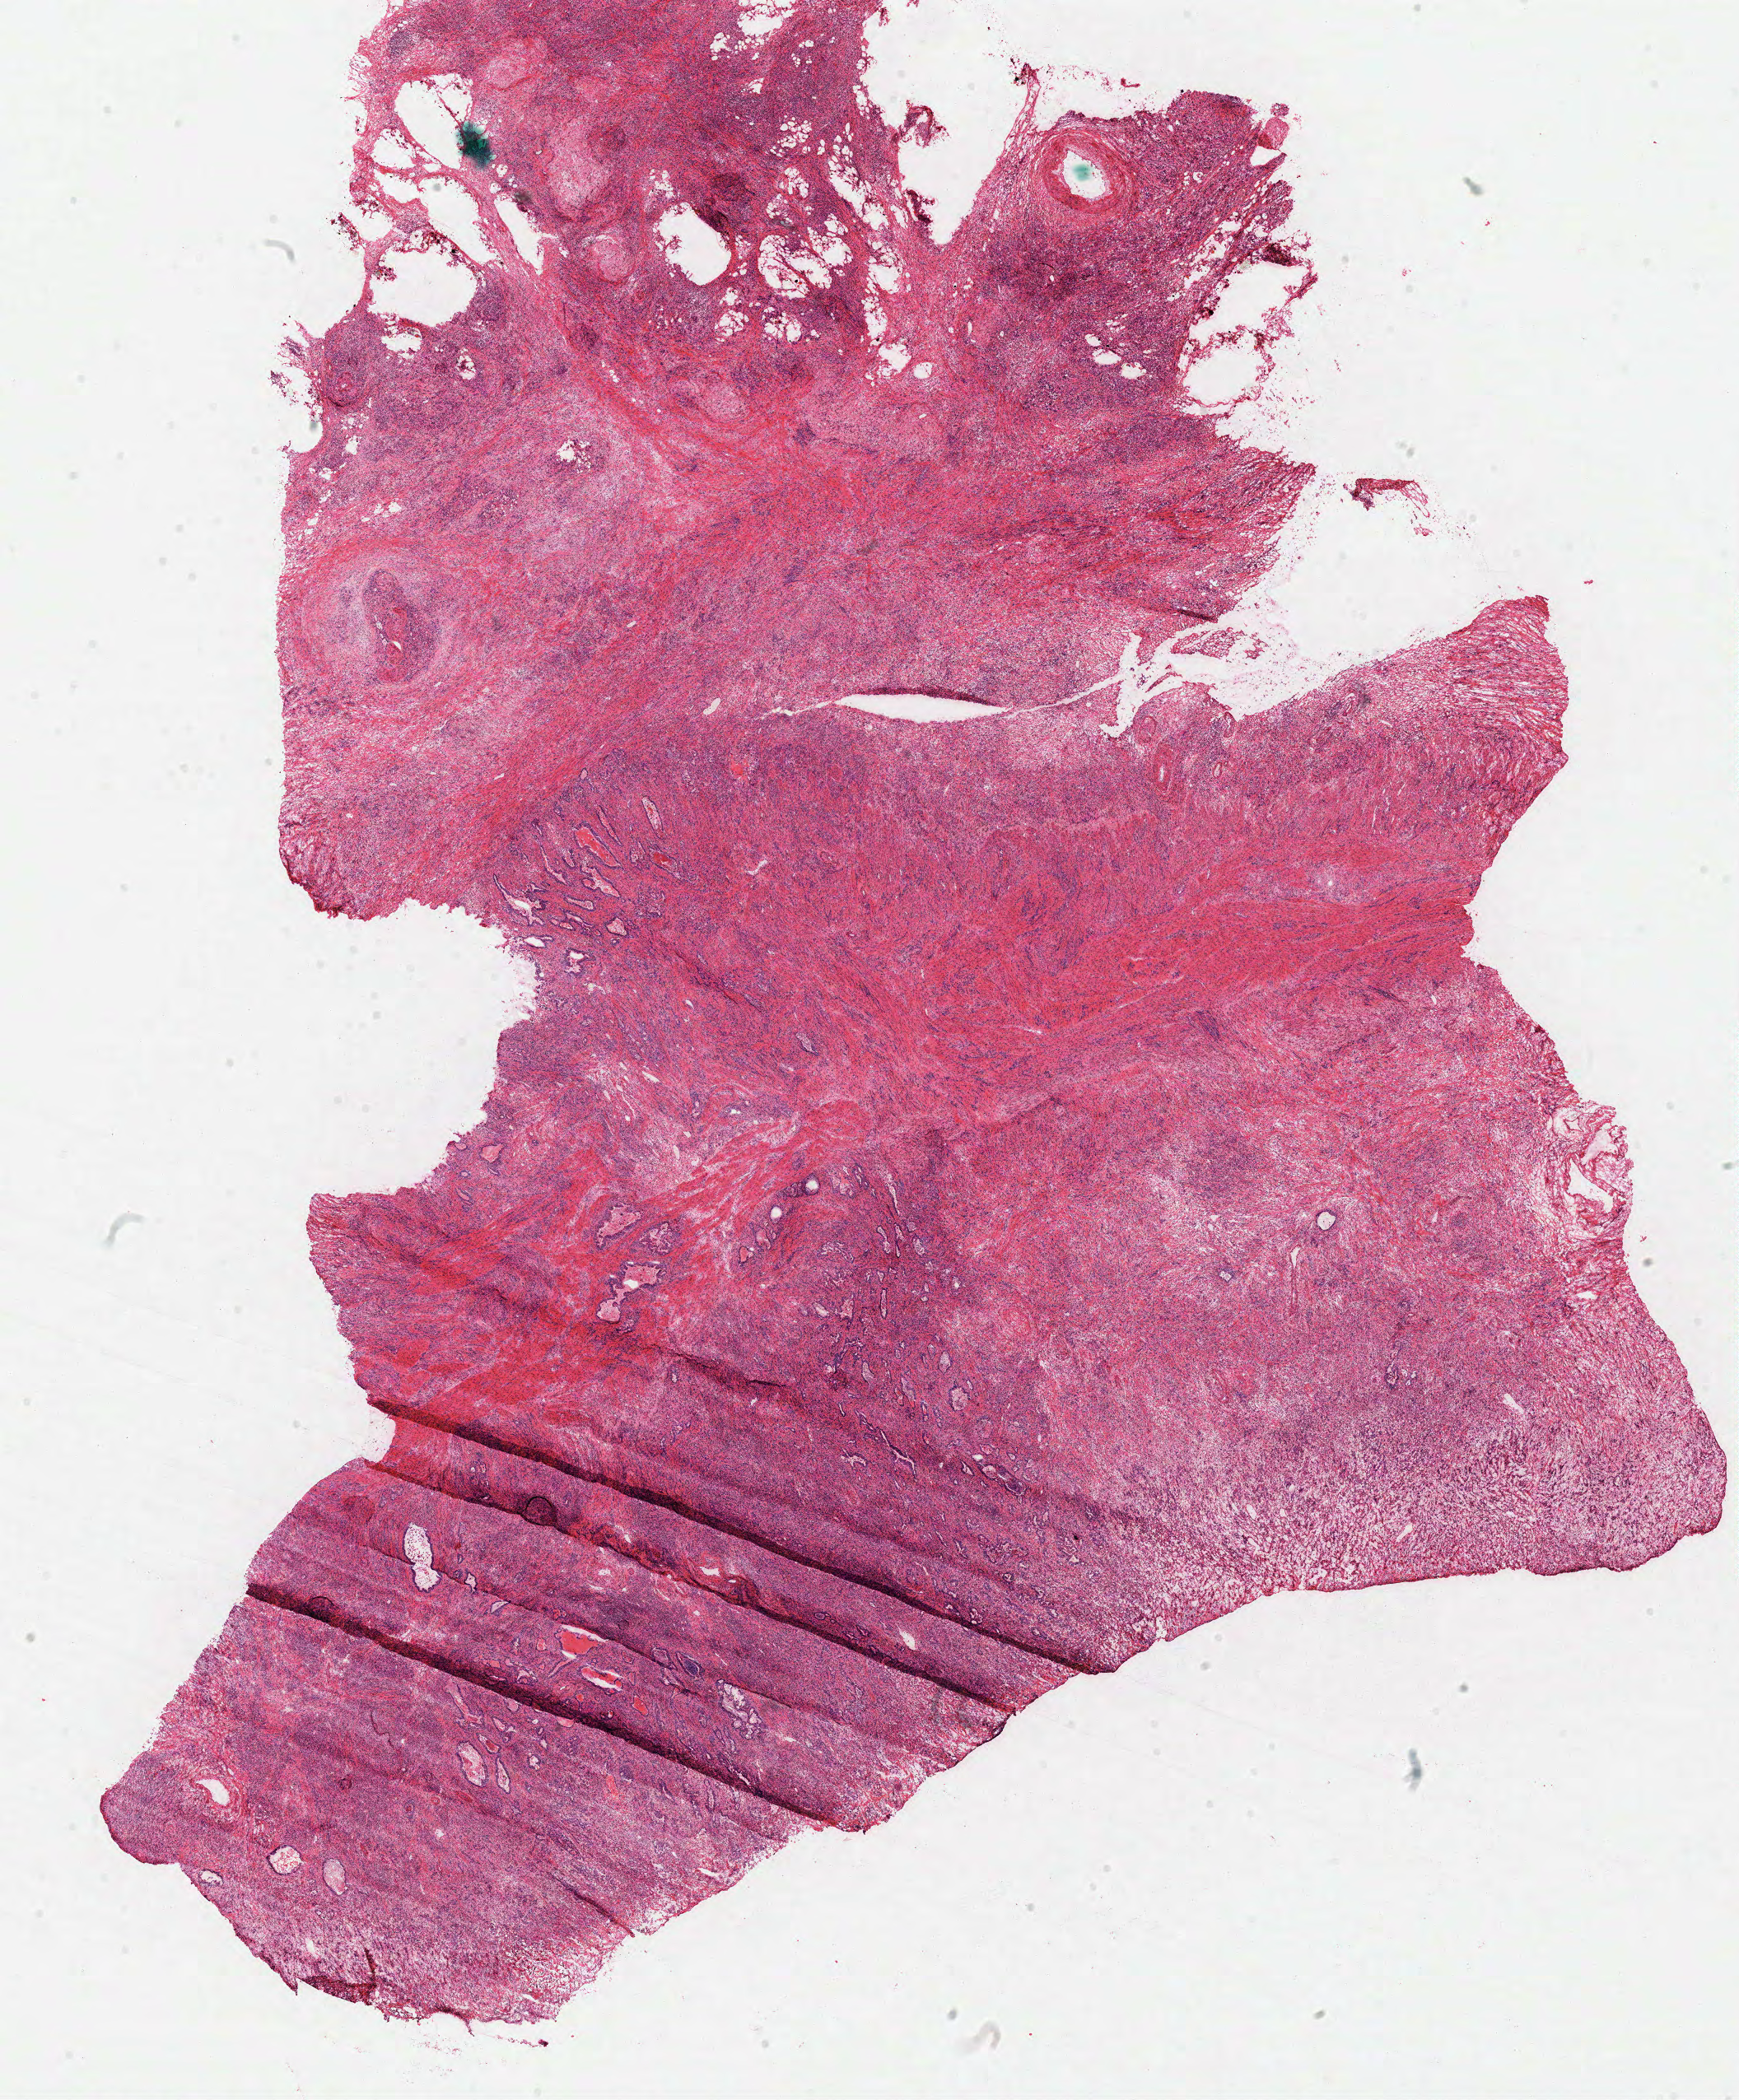
Digitized H&E-stained tissue section (whole slide), a low-resolution overview of the entire scanned area, about 16.6 x 20.1 mm (acquisition: 40x scan). Frozen section. Primary tumour sample from the stomach. Male, age 63 years at initial diagnosis. Histologic grade: G3 (poorly differentiated). Pathologist review of this section (percent, as recorded): tumour cells 75%, tumour nuclei 75%, normal cells 0%, stromal cells 20%, necrosis 5%.
Lymph nodes positive (case pathology): 5 of 15 examined. Pathologic diagnosis: Adenocarcinoma, NOS (cardia, NOS). TNM: T3 N1 M0. AJCC pathologic stage: IIIA.